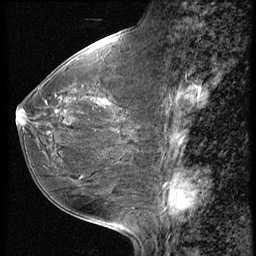
Breast MRI (dynamic contrast-enhanced), one sagittal slice; position 24 of 56 along the scan axis; 3 images stored at this slice position (order not interpretable as contrast timing); 1.5 T; TE 4.2 ms, TR 9 ms; 2.5 mm slice thickness; 256 × 256 image matrix, field of view 180 × 180 mm. Patient: female, 49 years. From the clinical record (not read from this slice): setting: breast cancer imaged before/during neoadjuvant chemotherapy; receptor status: HER2-positive.
Outlined on this slice (semi-automatic segmentation, software-assisted and operator-edited):
- analysis volume of interest (the breast-tissue region the enhancement analysis was run in; not a lesion): bounding box (x1, y1, x2, y2) in pixels: (17, 74, 148, 198)
- tumour enhancement mask (voxels above the 140 % enhancement threshold inside the analysis volume of interest): (17, 111, 58, 126)